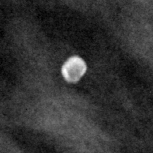
Cropped region of a digitized screen-film mammogram centred on a radiologist-marked abnormality, left breast, MLO view.
Finding: calcifications, morphology lucent center; BI-RADS assessment category 2; subtlety rating 3 on a 1 (subtle) to 5 (obvious) scale; benign; no additional work-up was recommended (benign without callback).